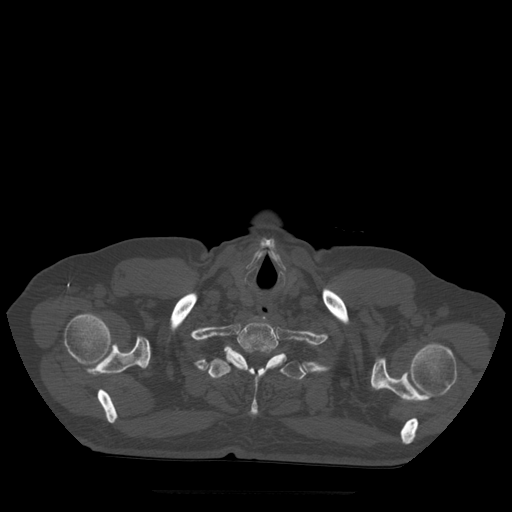
CT including the spine, one axial slice. Position 434 of 522 along the scan axis. Bone window (W 1800 / L 400 HU). 512 × 512 image matrix. Patient age 72 years. From the clinical record (not read from this slice): primary cancer: prostate.
Outlined on this slice (semi-automatically segmented with operator editing):
- T1 vertebra: bounding box (x1, y1, x2, y2) in pixels: (225, 321, 279, 367)
- T2 vertebra: (208, 346, 307, 416)